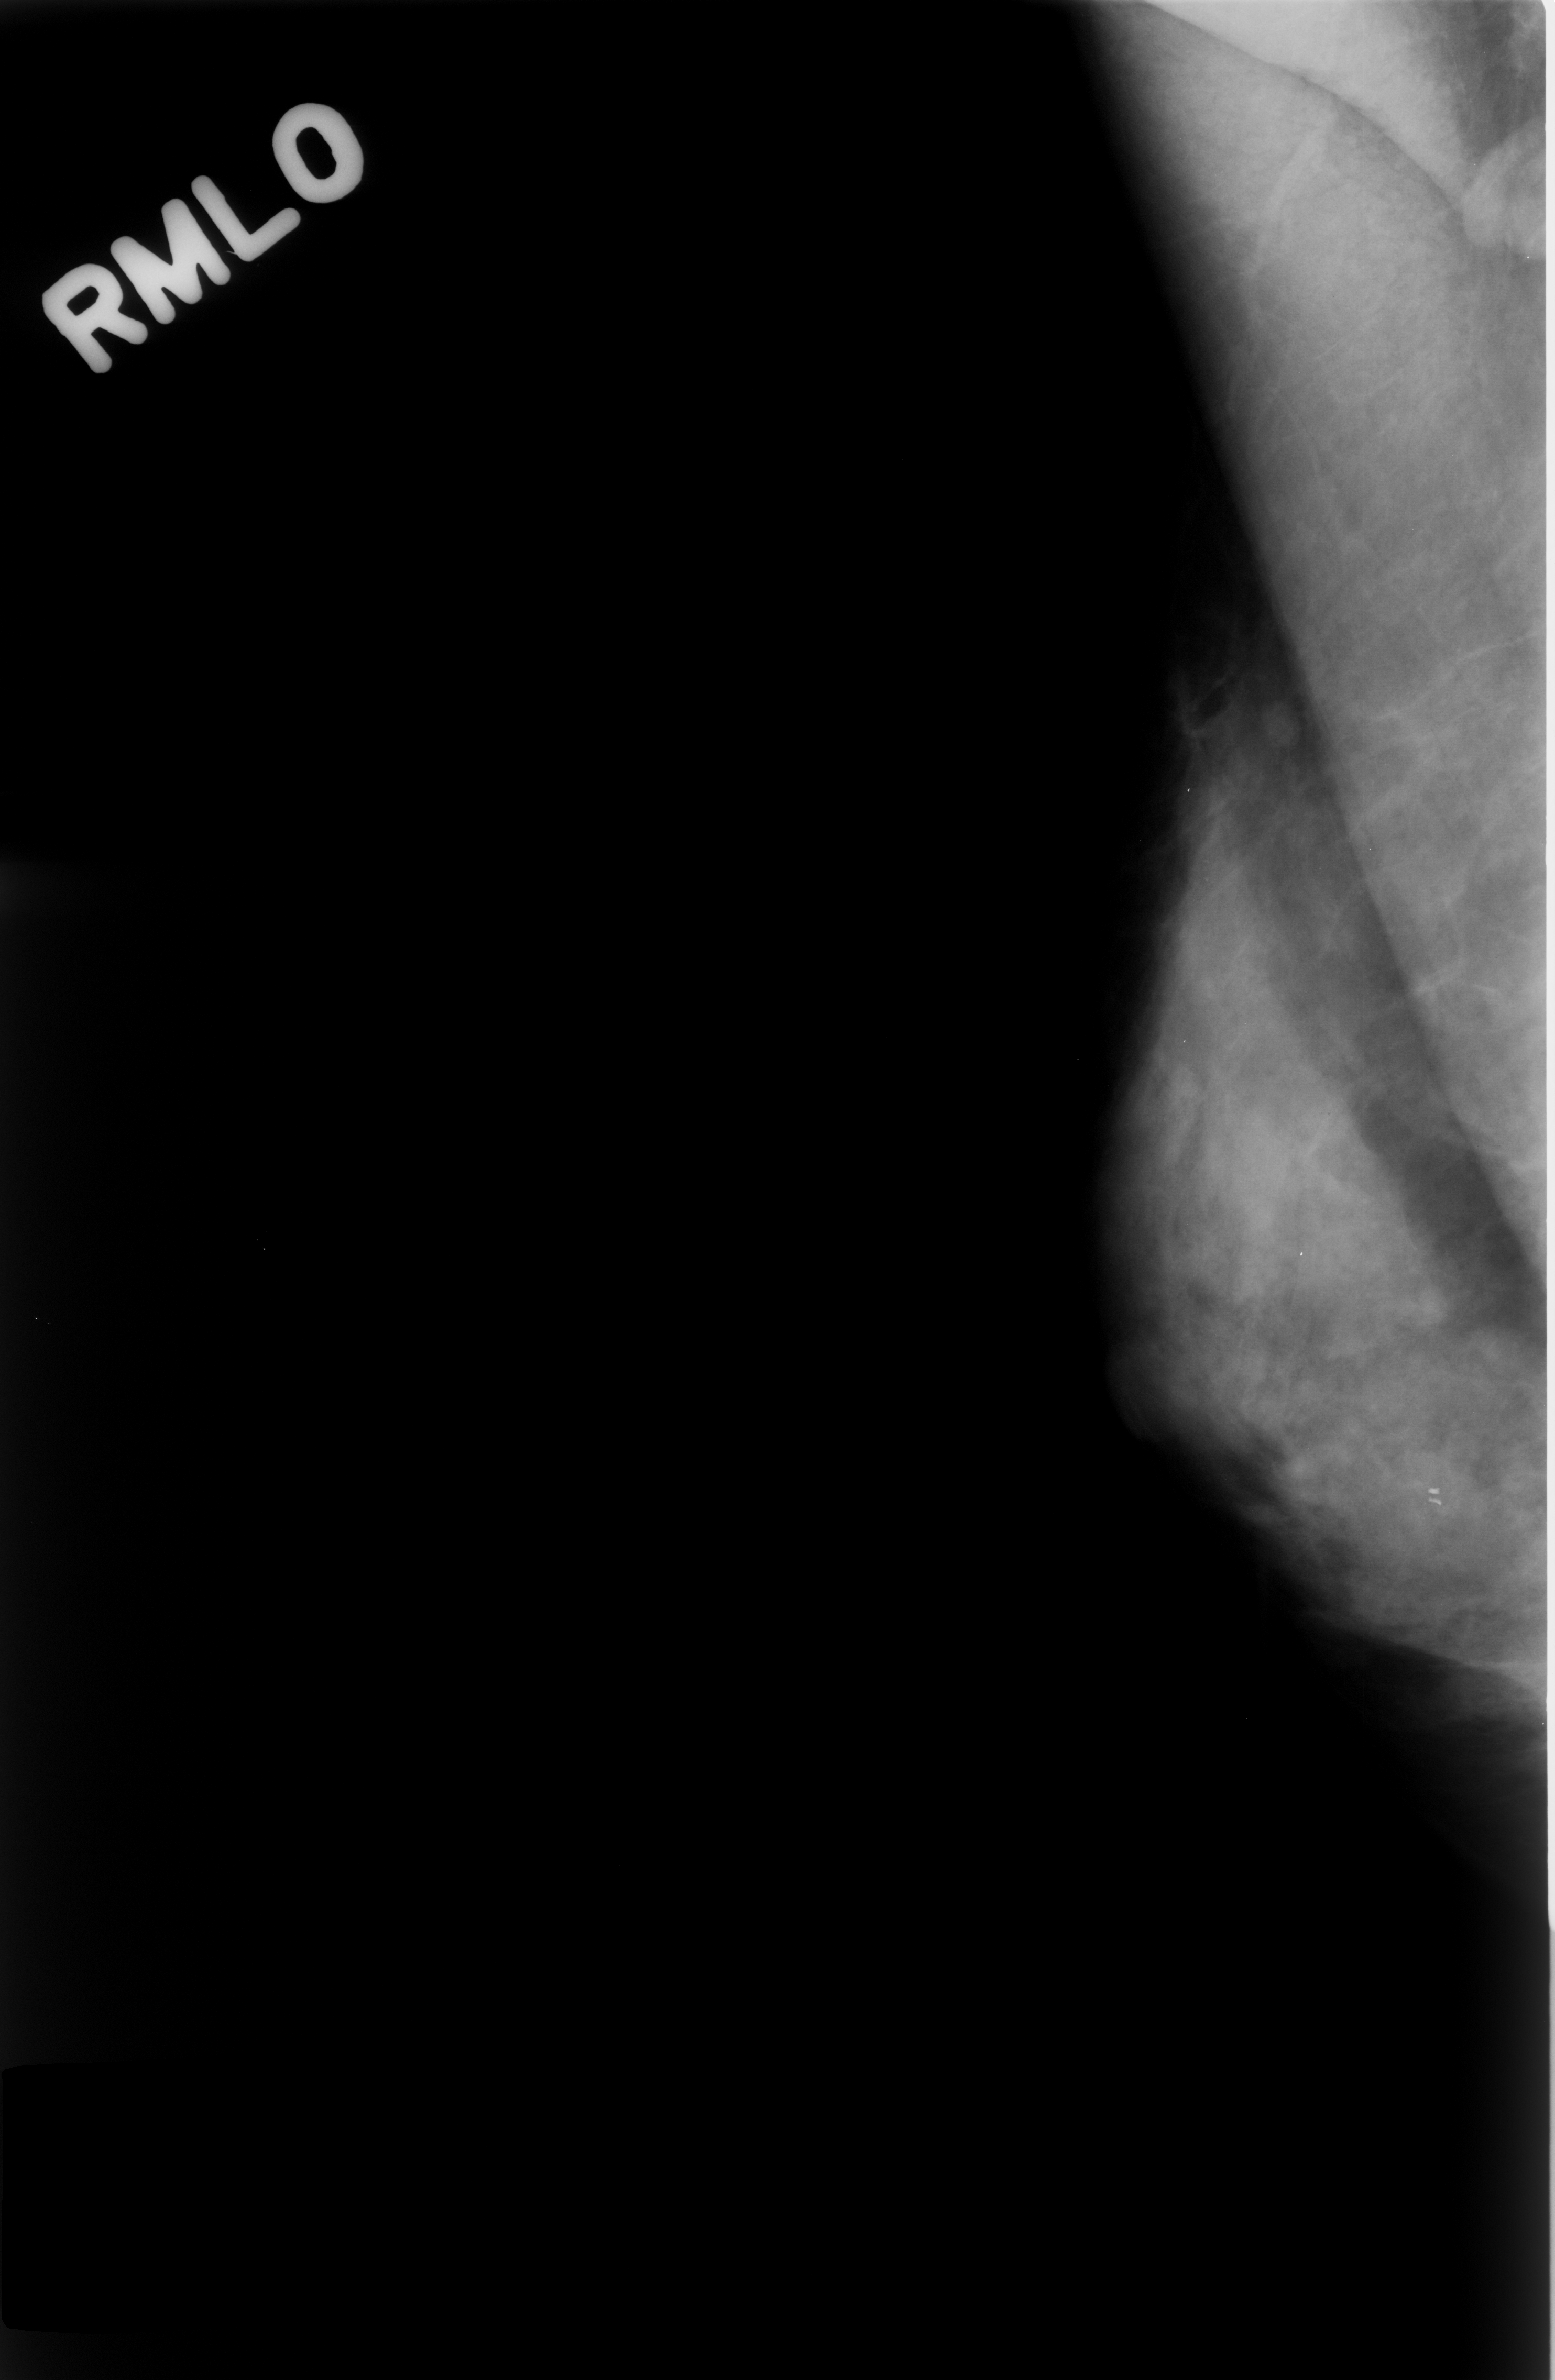
Digitized screen-film mammogram; right breast; MLO view; breast composition: extremely dense (BI-RADS density category 4 of 4).
- Finding: mass, shape oval, margins circumscribed; BI-RADS assessment category 3; subtlety rating 4 on a 1 (subtle) to 5 (obvious) scale; benign; no additional work-up was recommended (benign without callback).